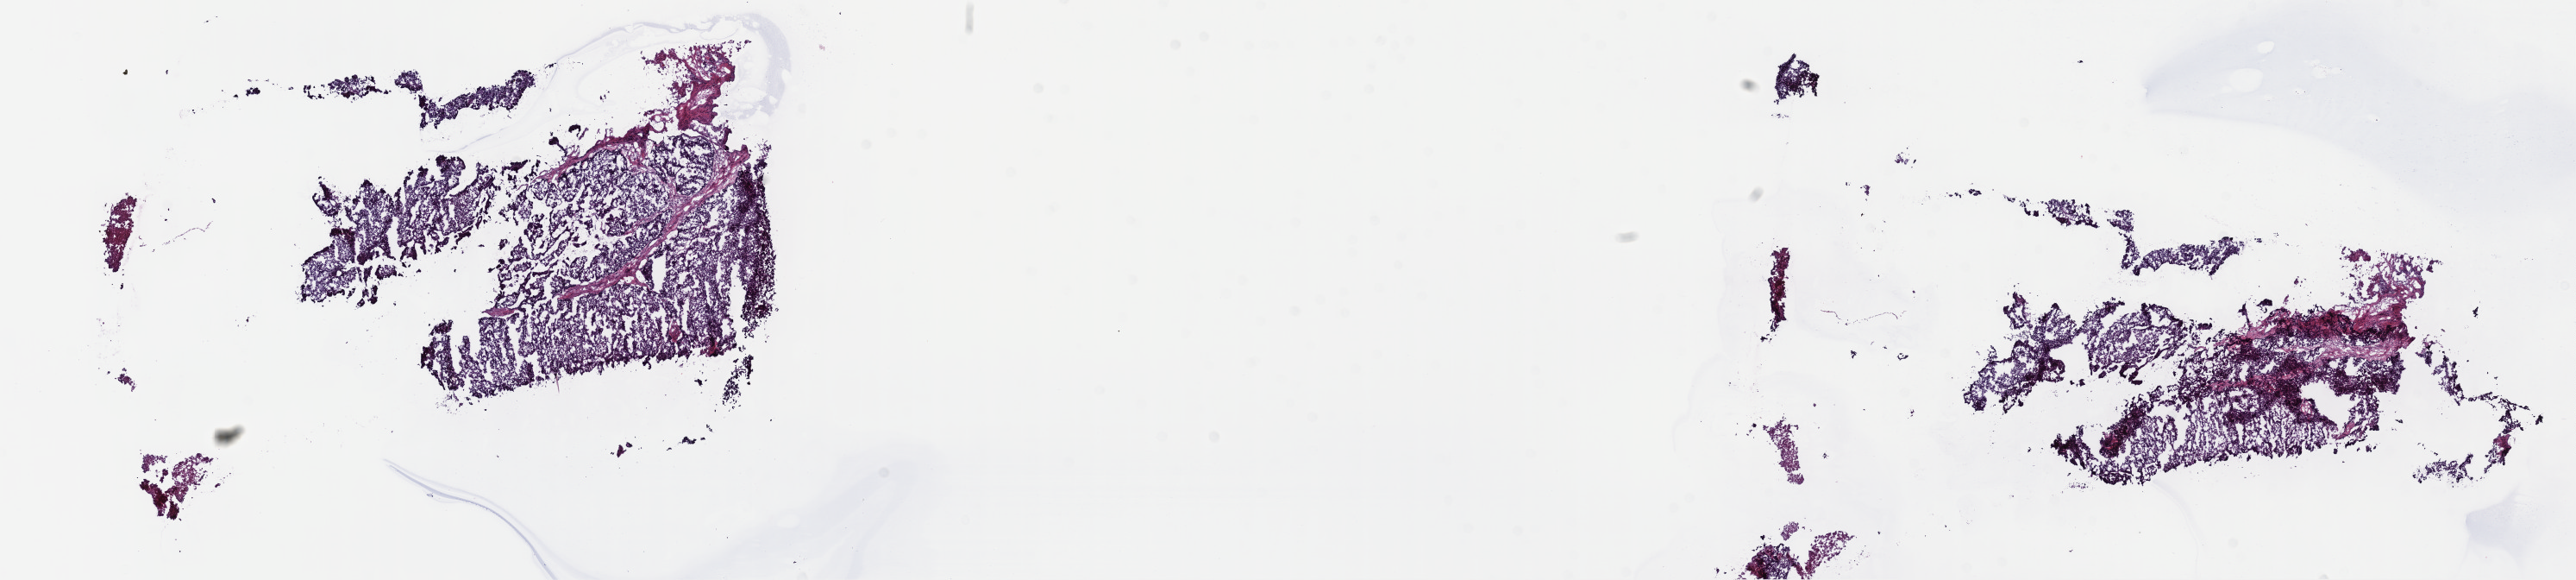
Hematoxylin and eosin (H&E) stained whole-slide image, low-resolution overview of the scanned area, about 24.2 x 5.4 mm. Frozen section from the top of the tissue portion. Primary tumour sample from the liver. Patient: female, age at initial diagnosis 53 years. Composition of this section per pathologist review: tumour cells 100%, tumour nuclei 80%.
Diagnosis: Hepatocellular carcinoma, NOS.